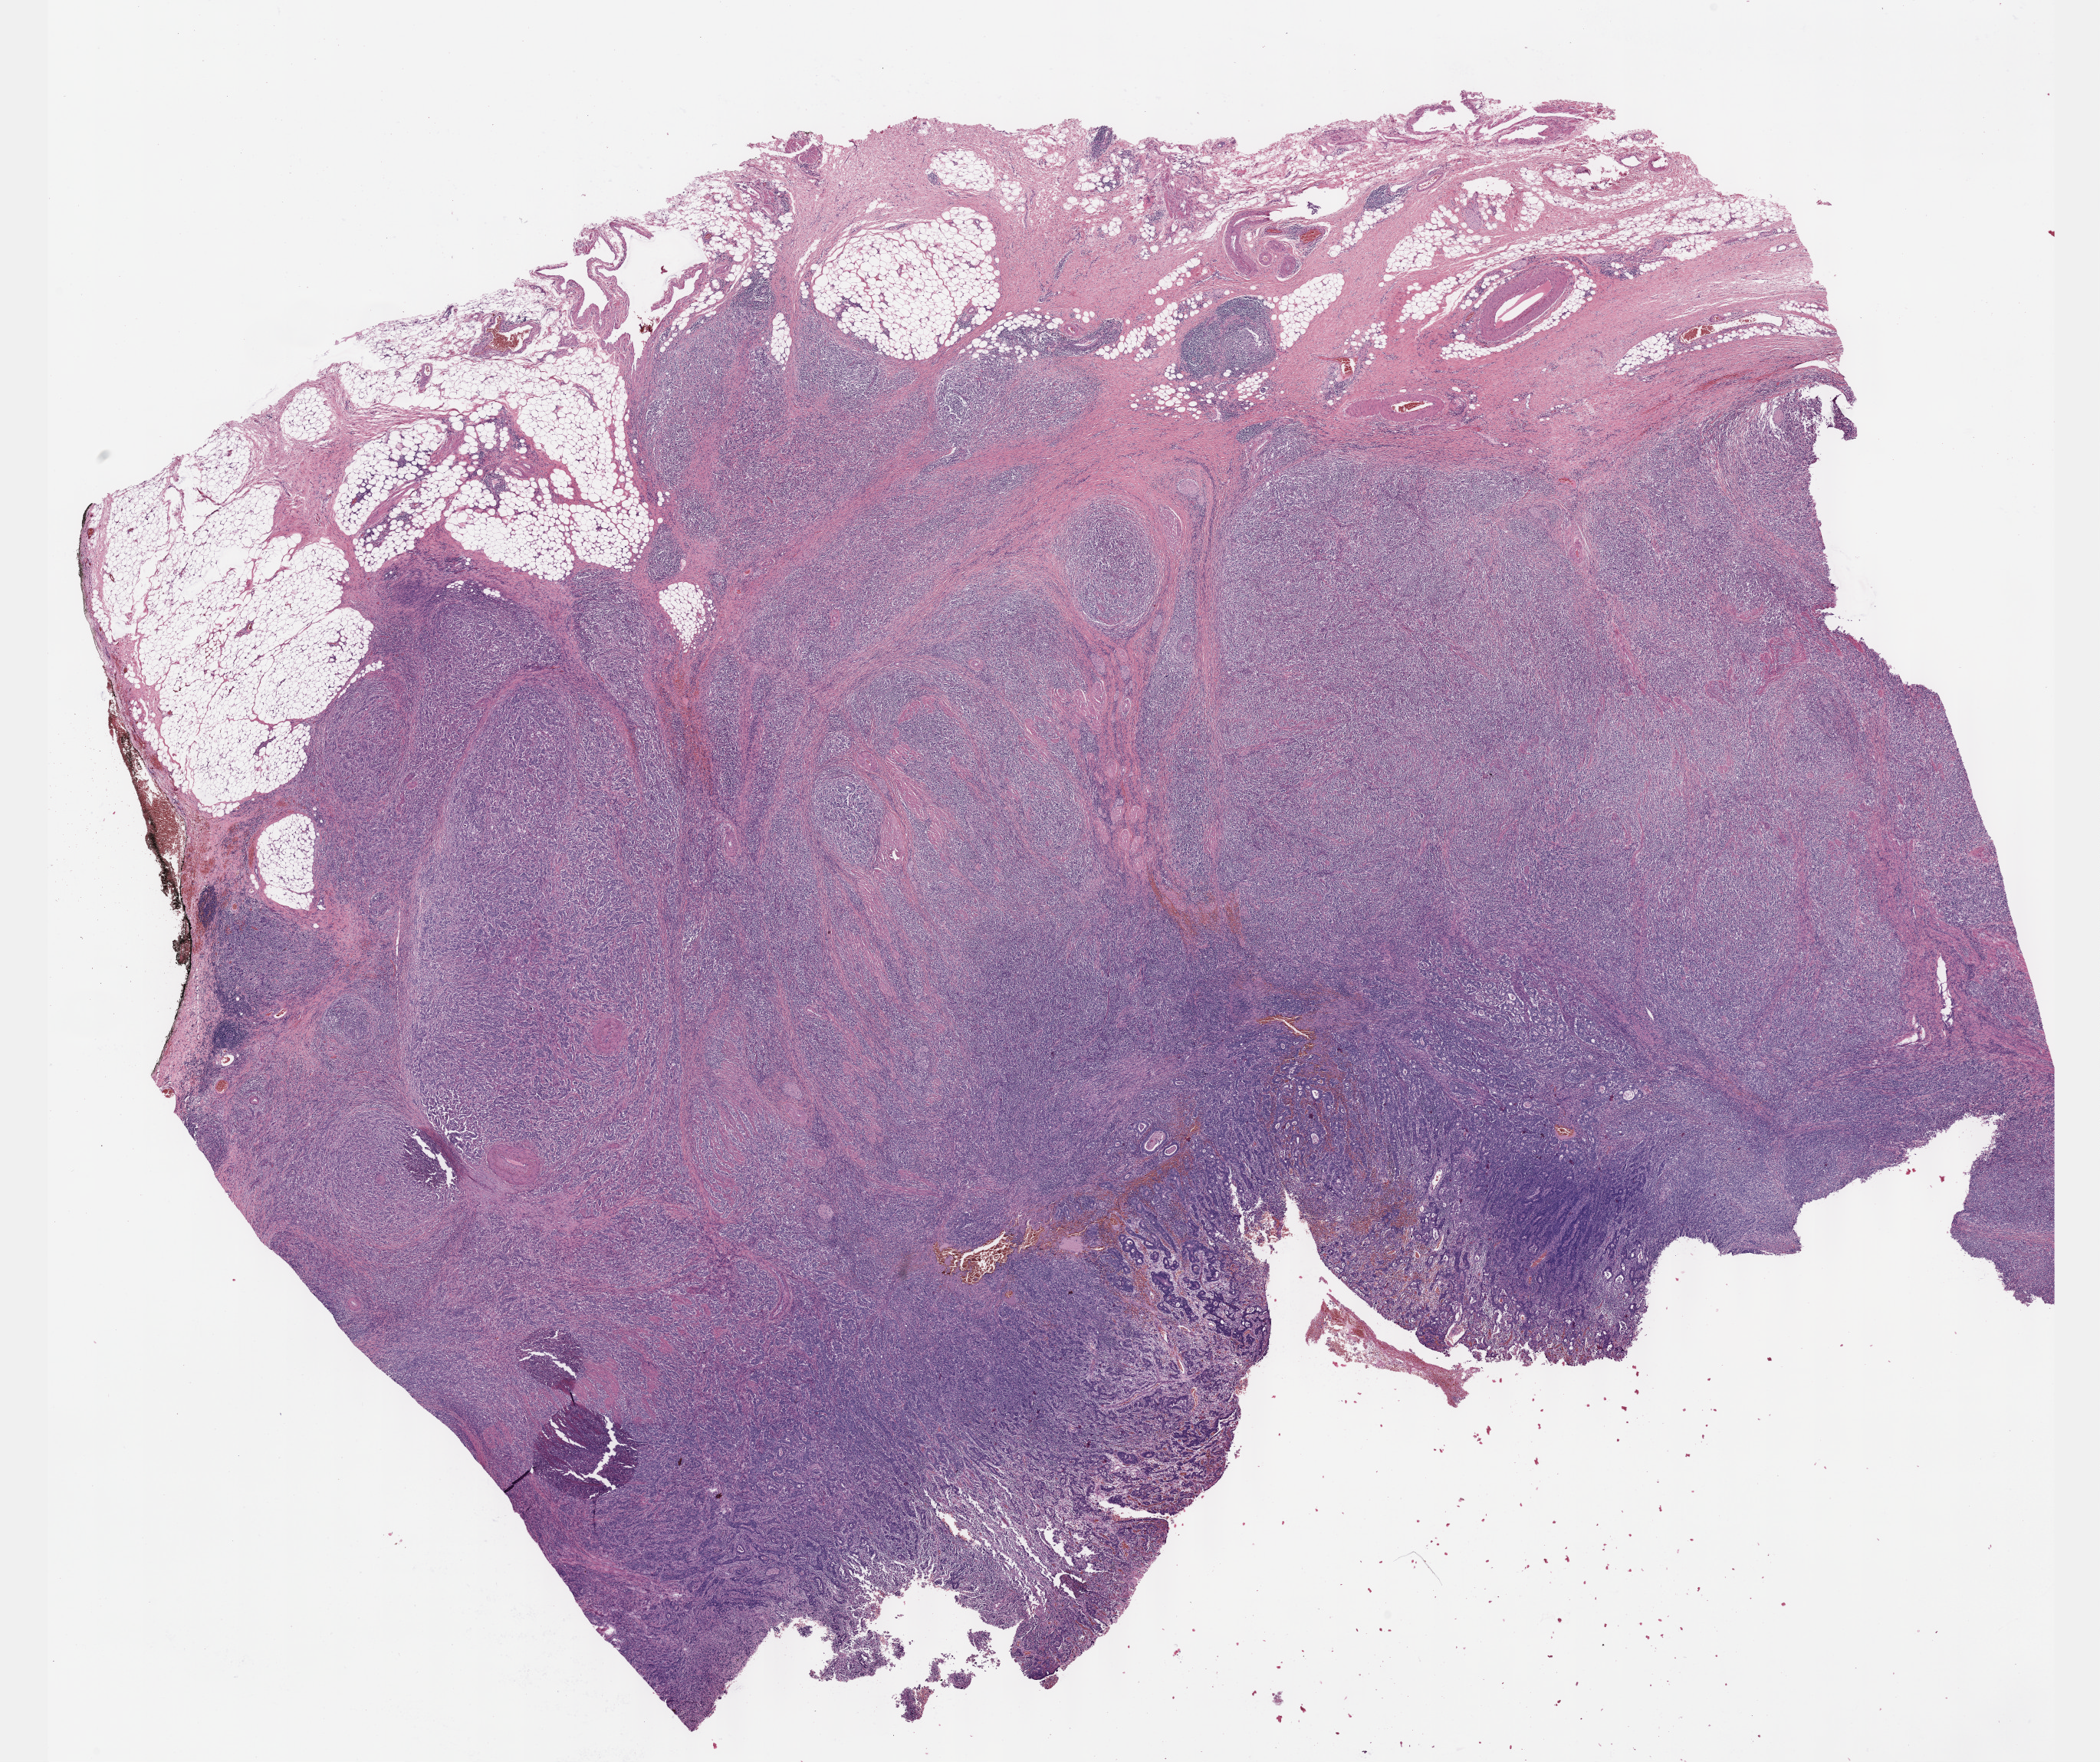
Whole-slide histology image, H&E-stained — shown as a low-resolution overview of the whole scanned area (about 22.1 x 18.6 mm, acquisition: 40x scan); formalin-fixed paraffin-embedded (FFPE) diagnostic section; sample: primary tumour, stomach. Patient sex: male. Histologic grade: G3 (poorly differentiated).
- TNM: T3 N1 M0
- AJCC pathologic stage: IIIA (6th edition)
- lymph nodes positive (case pathology): 4 of 12 examined
- histologic diagnosis: Tubular adenocarcinoma